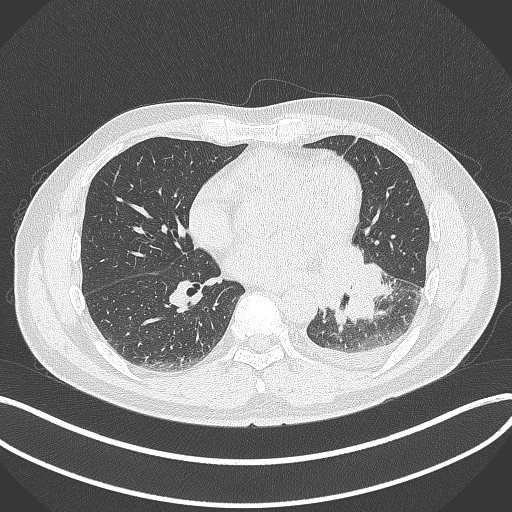
Chest CT, one axial slice; position 158 of 342 along the scan axis; reconstruction kernel B70f; 120 kVp; lung window (W 1500 / L -600 HU); 1 mm slice thickness; 512 × 512 image matrix. Male patient, age 58 years. From the clinical record (not read from this slice): clinical TNM (as recorded): T3 N1 M1b.
Annotated regions visible in this slice (rectangle marked by the reading radiologist):
- lung tumour (recorded histology: small cell carcinoma): bounding box (x1, y1, x2, y2) in pixels: (319, 241, 386, 324)